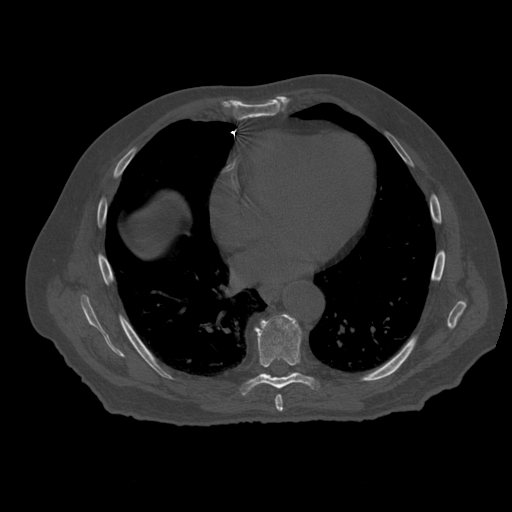
CT including the spine, one axial slice. Position 342 of 399 along the scan axis. Reconstruction kernel STANDARD. Bone window (W 1800 / L 400 HU). 1.25 mm slice thickness. 512 × 512 image matrix. Patient age 73 years. Case-level facts recorded for this patient, not image findings: primary cancer: prostate; vertebrae with lytic lesions (as recorded): L2.
Structures marked on this image (semi-automatic segmentation, software-assisted and operator-edited):
- T7 vertebra: box from (x=275, y=395) to (x=283, y=413) px
- T8 vertebra: (x=243, y=314)–(x=314, y=395)